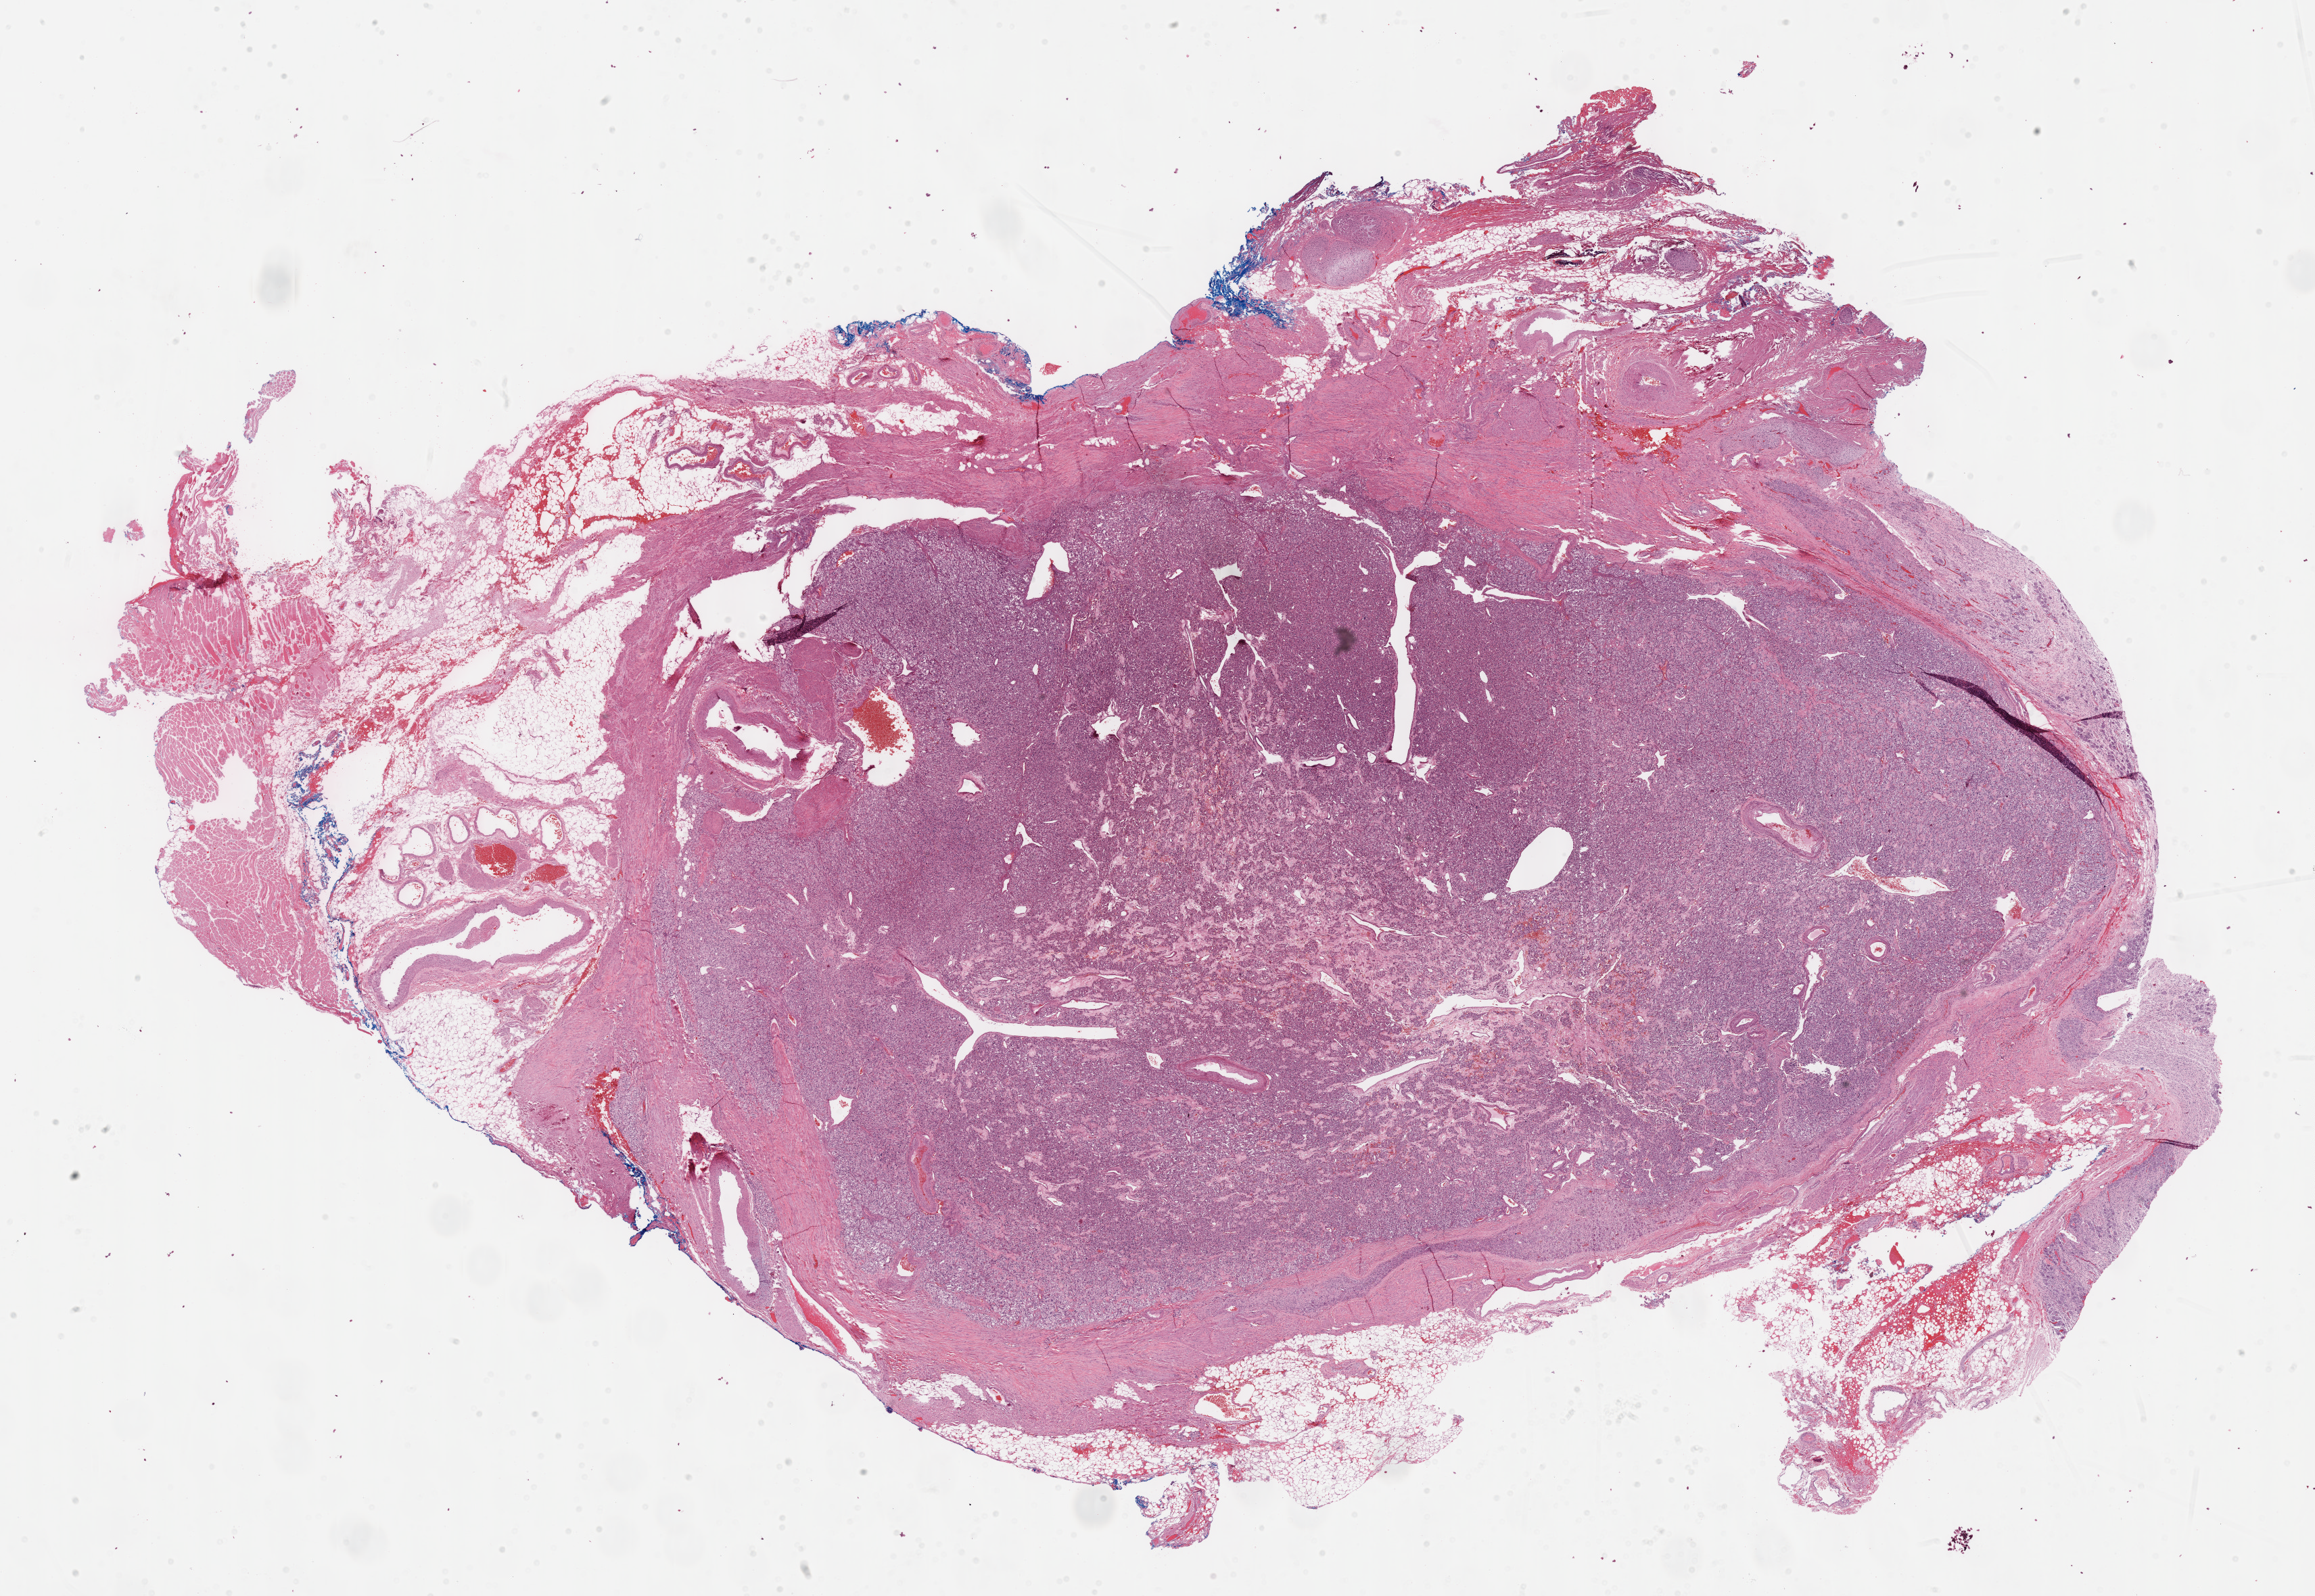
H&E-stained whole-slide image, shown as a low-resolution overview of the whole scanned area (about 27.7 x 19.1 mm, acquisition: 40x scan), formalin-fixed paraffin-embedded (FFPE) diagnostic section, sample: primary tumour, retroperitoneum and peritoneum. Female, age 72 years at initial diagnosis.
Pathologic diagnosis: Extra-adrenal paraganglioma, NOS (retroperitoneum).